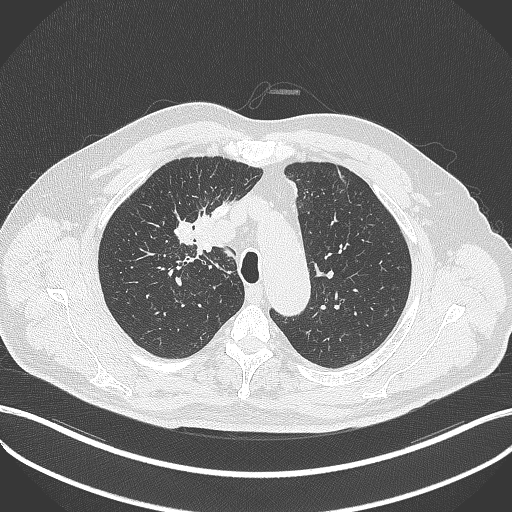
Chest CT, one axial slice; position 298 of 411 along the scan axis; lung window (W 1500 / L -600 HU); 1 mm slice thickness; 512 × 512 image matrix, field of view 400 × 400 mm. Patient: male, 60 years. From the clinical record (not read from this slice): clinical TNM (as recorded): T1b N1 M0.
Outlined on this slice (rectangle marked by the reading radiologist):
- lung tumour (recorded histology: squamous cell carcinoma): bounding box [x1, y1, x2, y2] px = [190, 214, 218, 257]